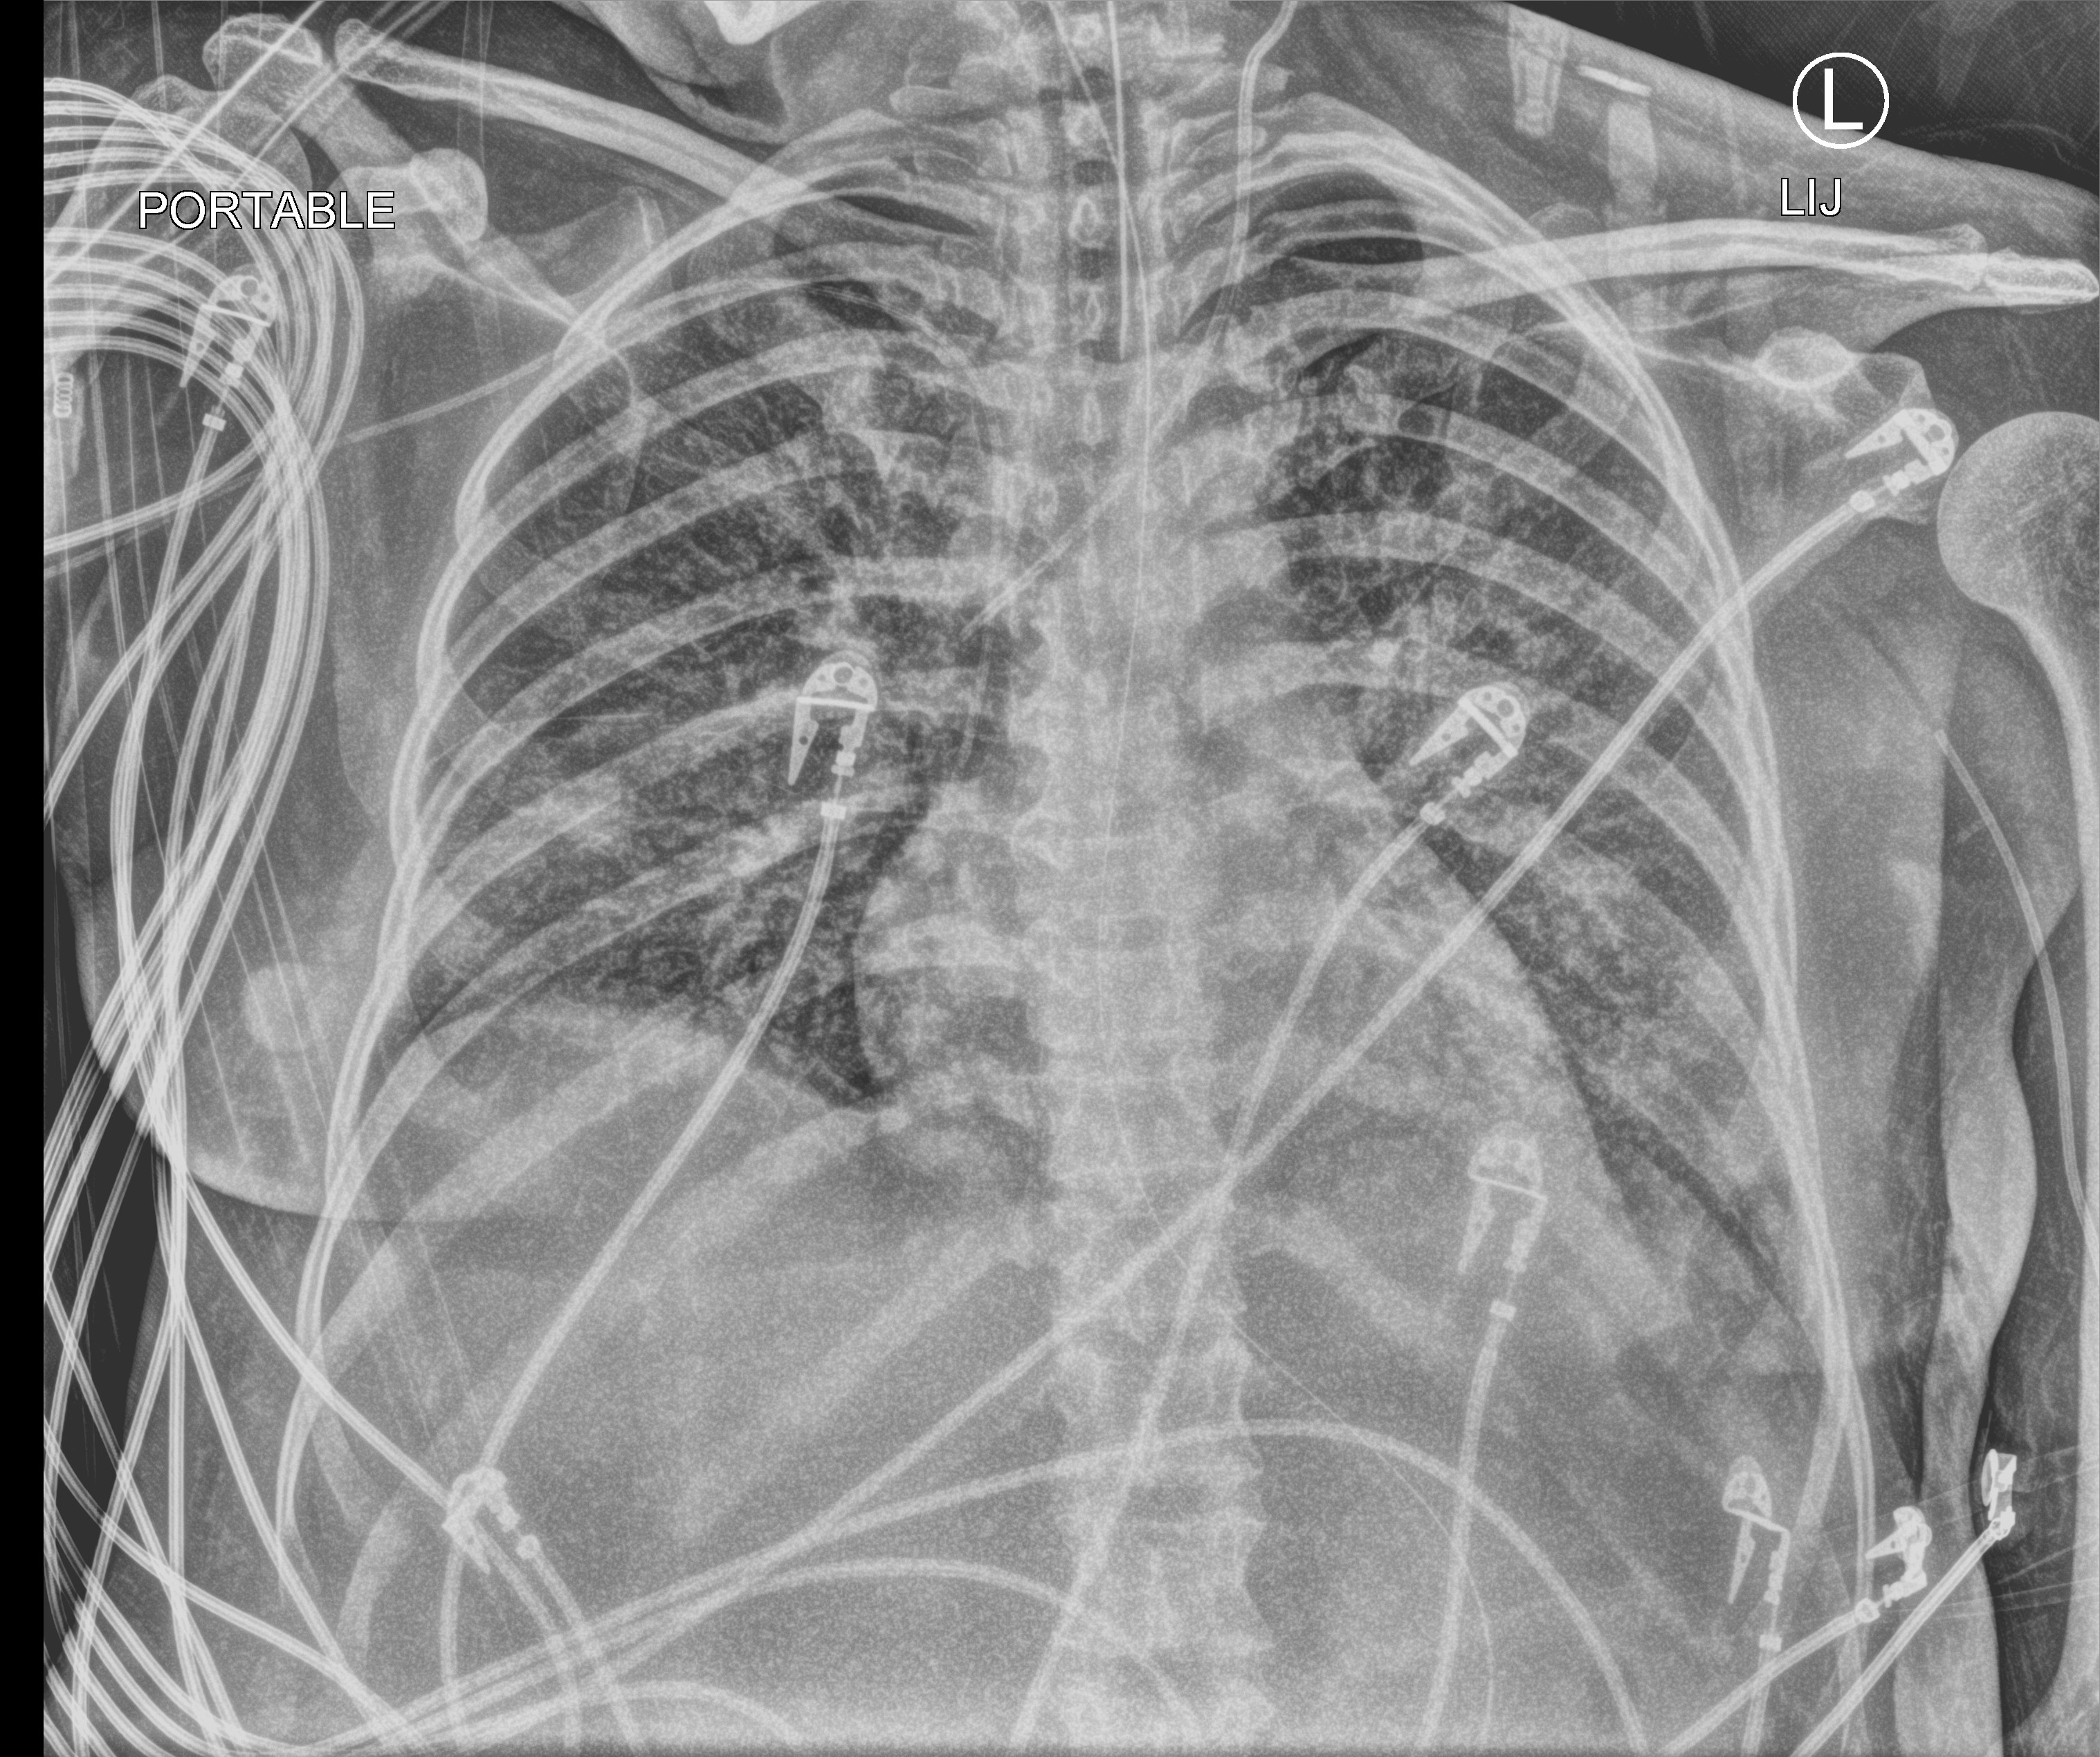
Chest X-ray (portable). Patient hospitalised with COVID-19; female, aged 18–59 years.
From the hospital-stay record, not from the radiograph (when in the stay this image was taken is not recorded):
- diabetes (admission record): no
- mechanically ventilated during this hospital stay: yes
- other chronic lung disease (admission record): no